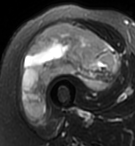
MRI of an extremity soft-tissue mass, one axial slice. Position 40 of 95 along the scan axis. T2-weighted fat-saturated. MR volume resampled by the dataset authors to the PET/CT grid (not the native acquisition matrix). 3.27 mm slice thickness. 135 × 146 image matrix, field of view 132 × 143 mm. Female patient. Case-level facts recorded for this patient, not image findings: histological type: pleiomorphic undifferentiated sarcoma; grade: high; site of the primary tumour: right quadricep.
Structures marked on this image (expert contour drawn on MRI and transferred to this co-registered scan by the dataset authors):
- gross tumour volume including surrounding oedema: bounding box [x1, y1, x2, y2] px = [21, 24, 120, 117]
- gross tumour volume (mass): [21, 24, 120, 117]